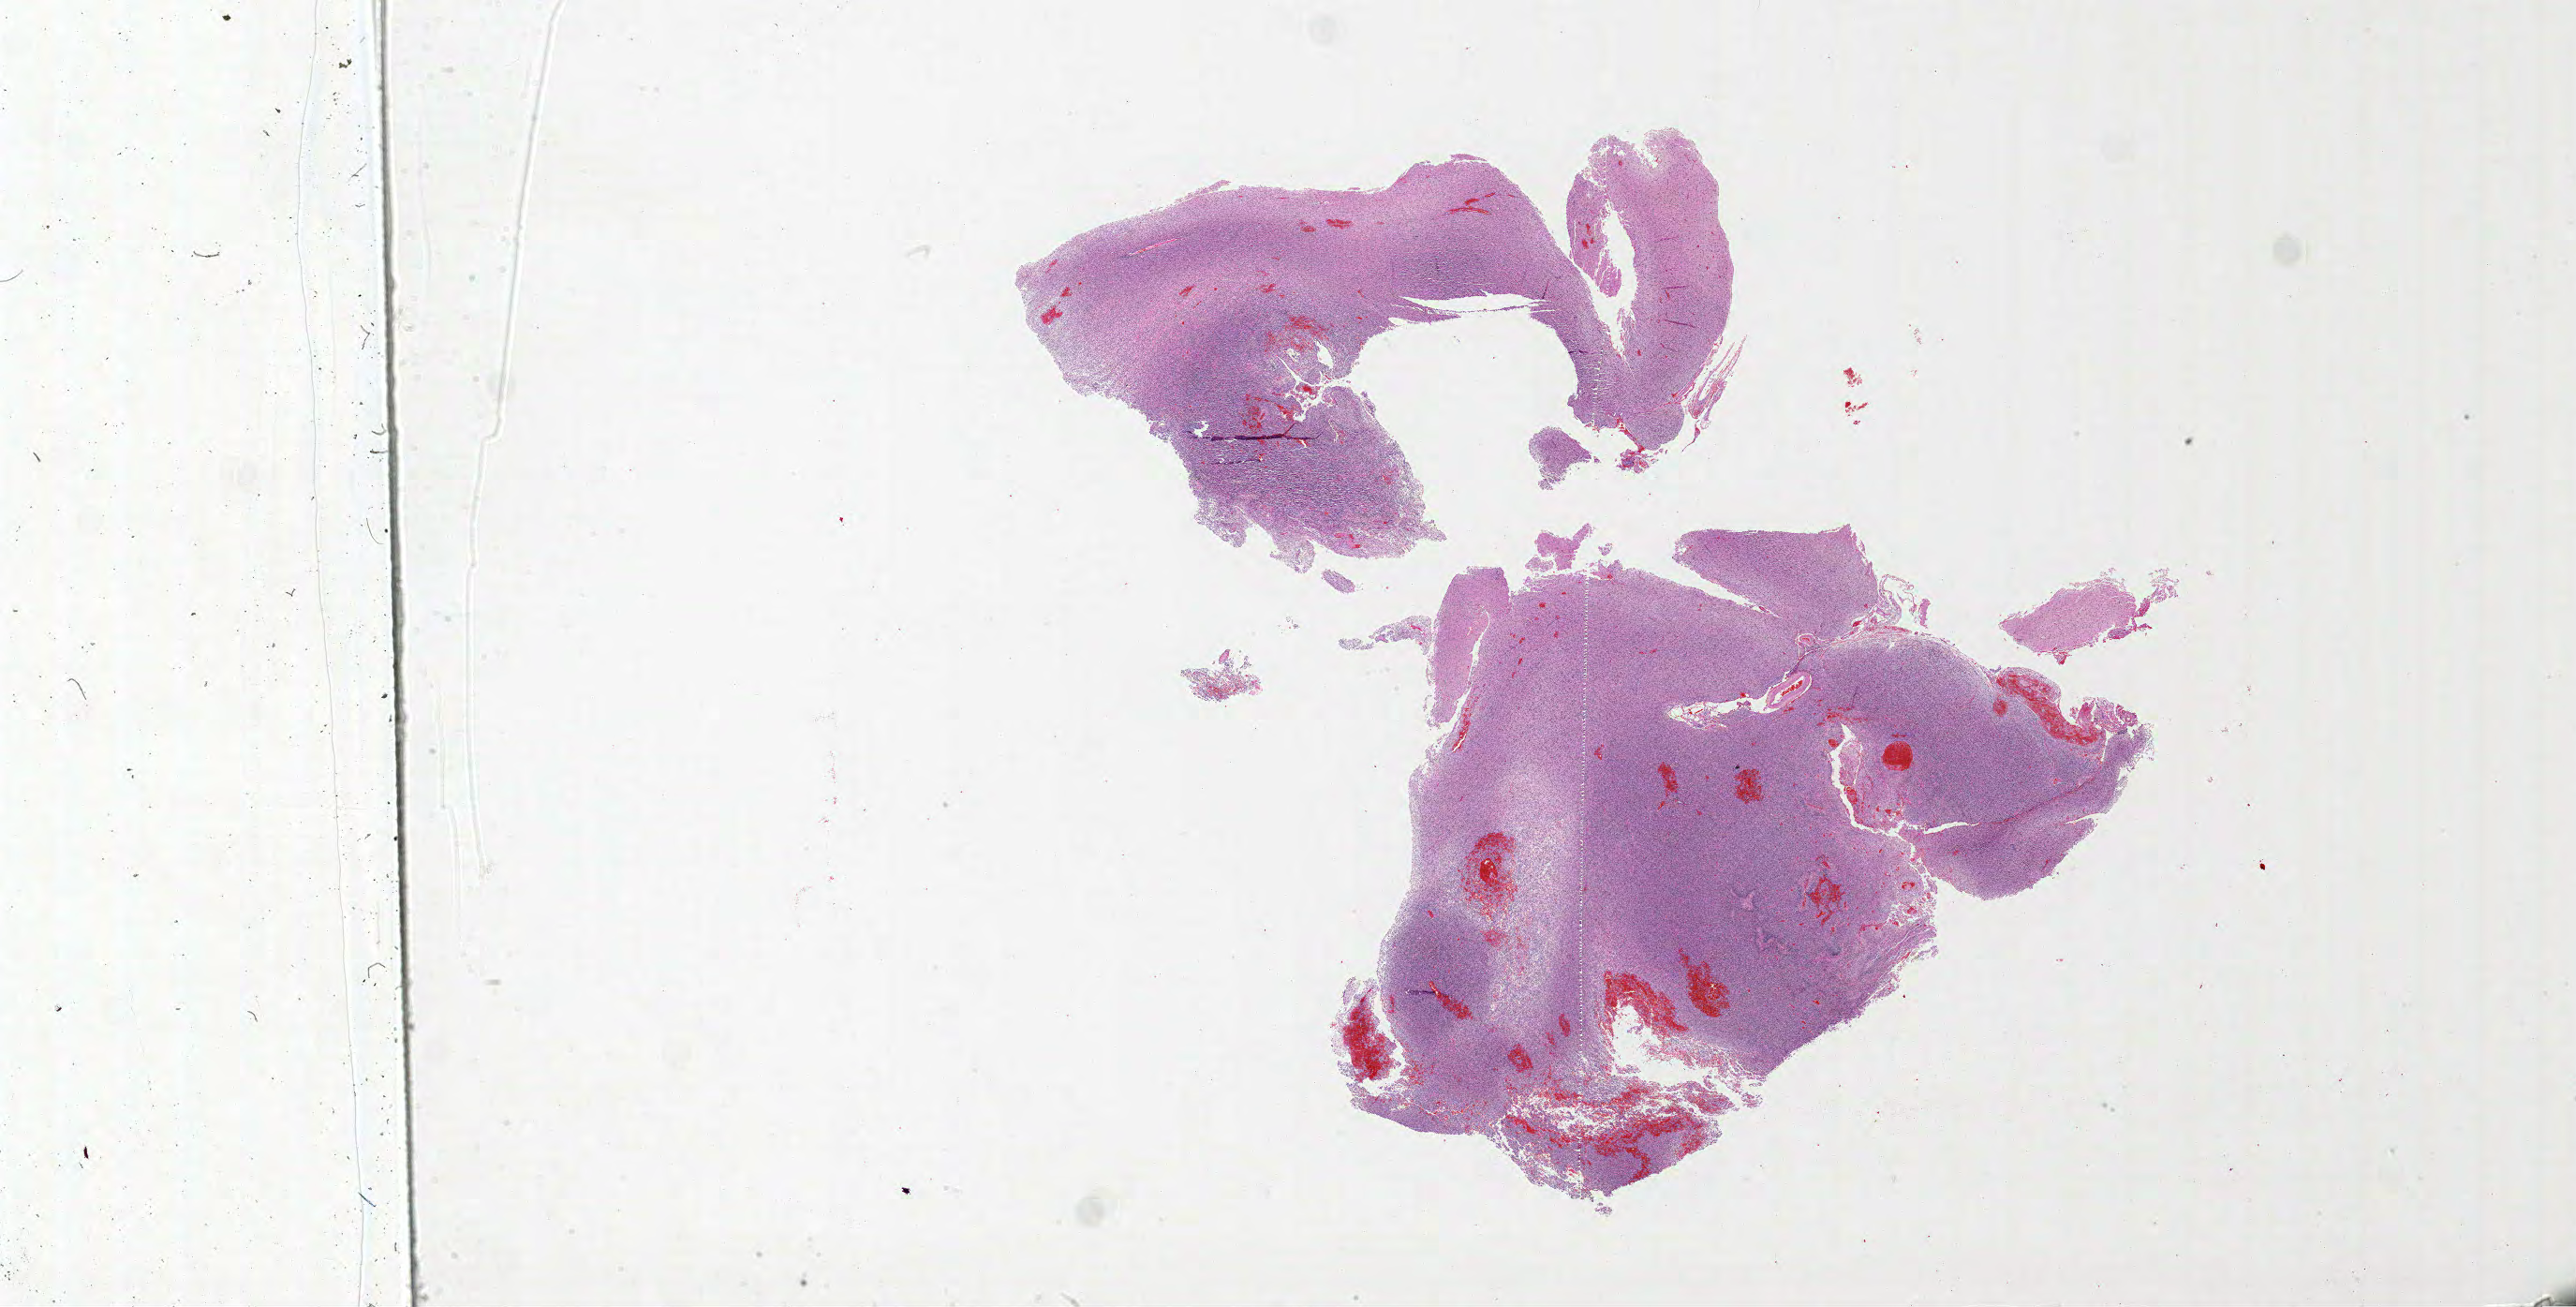
Digitized Hematoxylin and eosin (H&E) stained tissue section (whole slide), low-resolution overview of the scanned area, about 44.0 x 22.3 mm (slide scanned at 20x), formalin-fixed paraffin-embedded (FFPE) diagnostic section, primary tumour sample from the brain. Female, age 10 years at initial diagnosis.
Diagnosis: Glioblastoma.